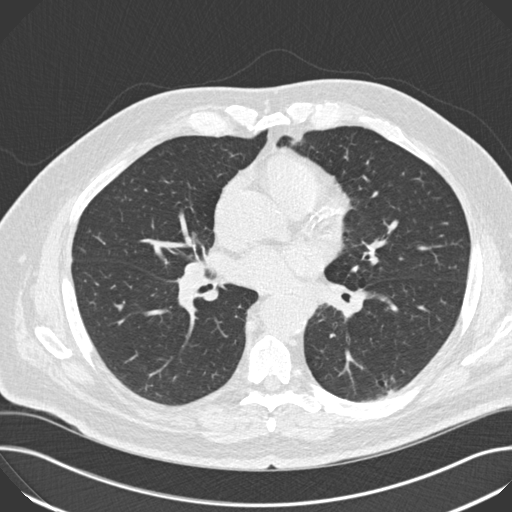
Axial slice from a low-dose chest CT screening exam; third screening round (two years after baseline); lung window (W 1500 / L -600 HU); slice 82 of 172 in the series. Male, age 68 years at enrolment. Current smoker at enrolment.
Lesion marked by an expert reader, box from (x=153, y=237) to (x=234, y=311) px. No non-calcified nodule or mass ≥4 mm was recorded by the screening reader at this exam. Official screen result: negative screen, no significant abnormalities. Later outcome: lung cancer diagnosed 151 days after this screen — small cell carcinoma, NOS, right hilum, mediastinum, stage IV (AJCC 6th edition).